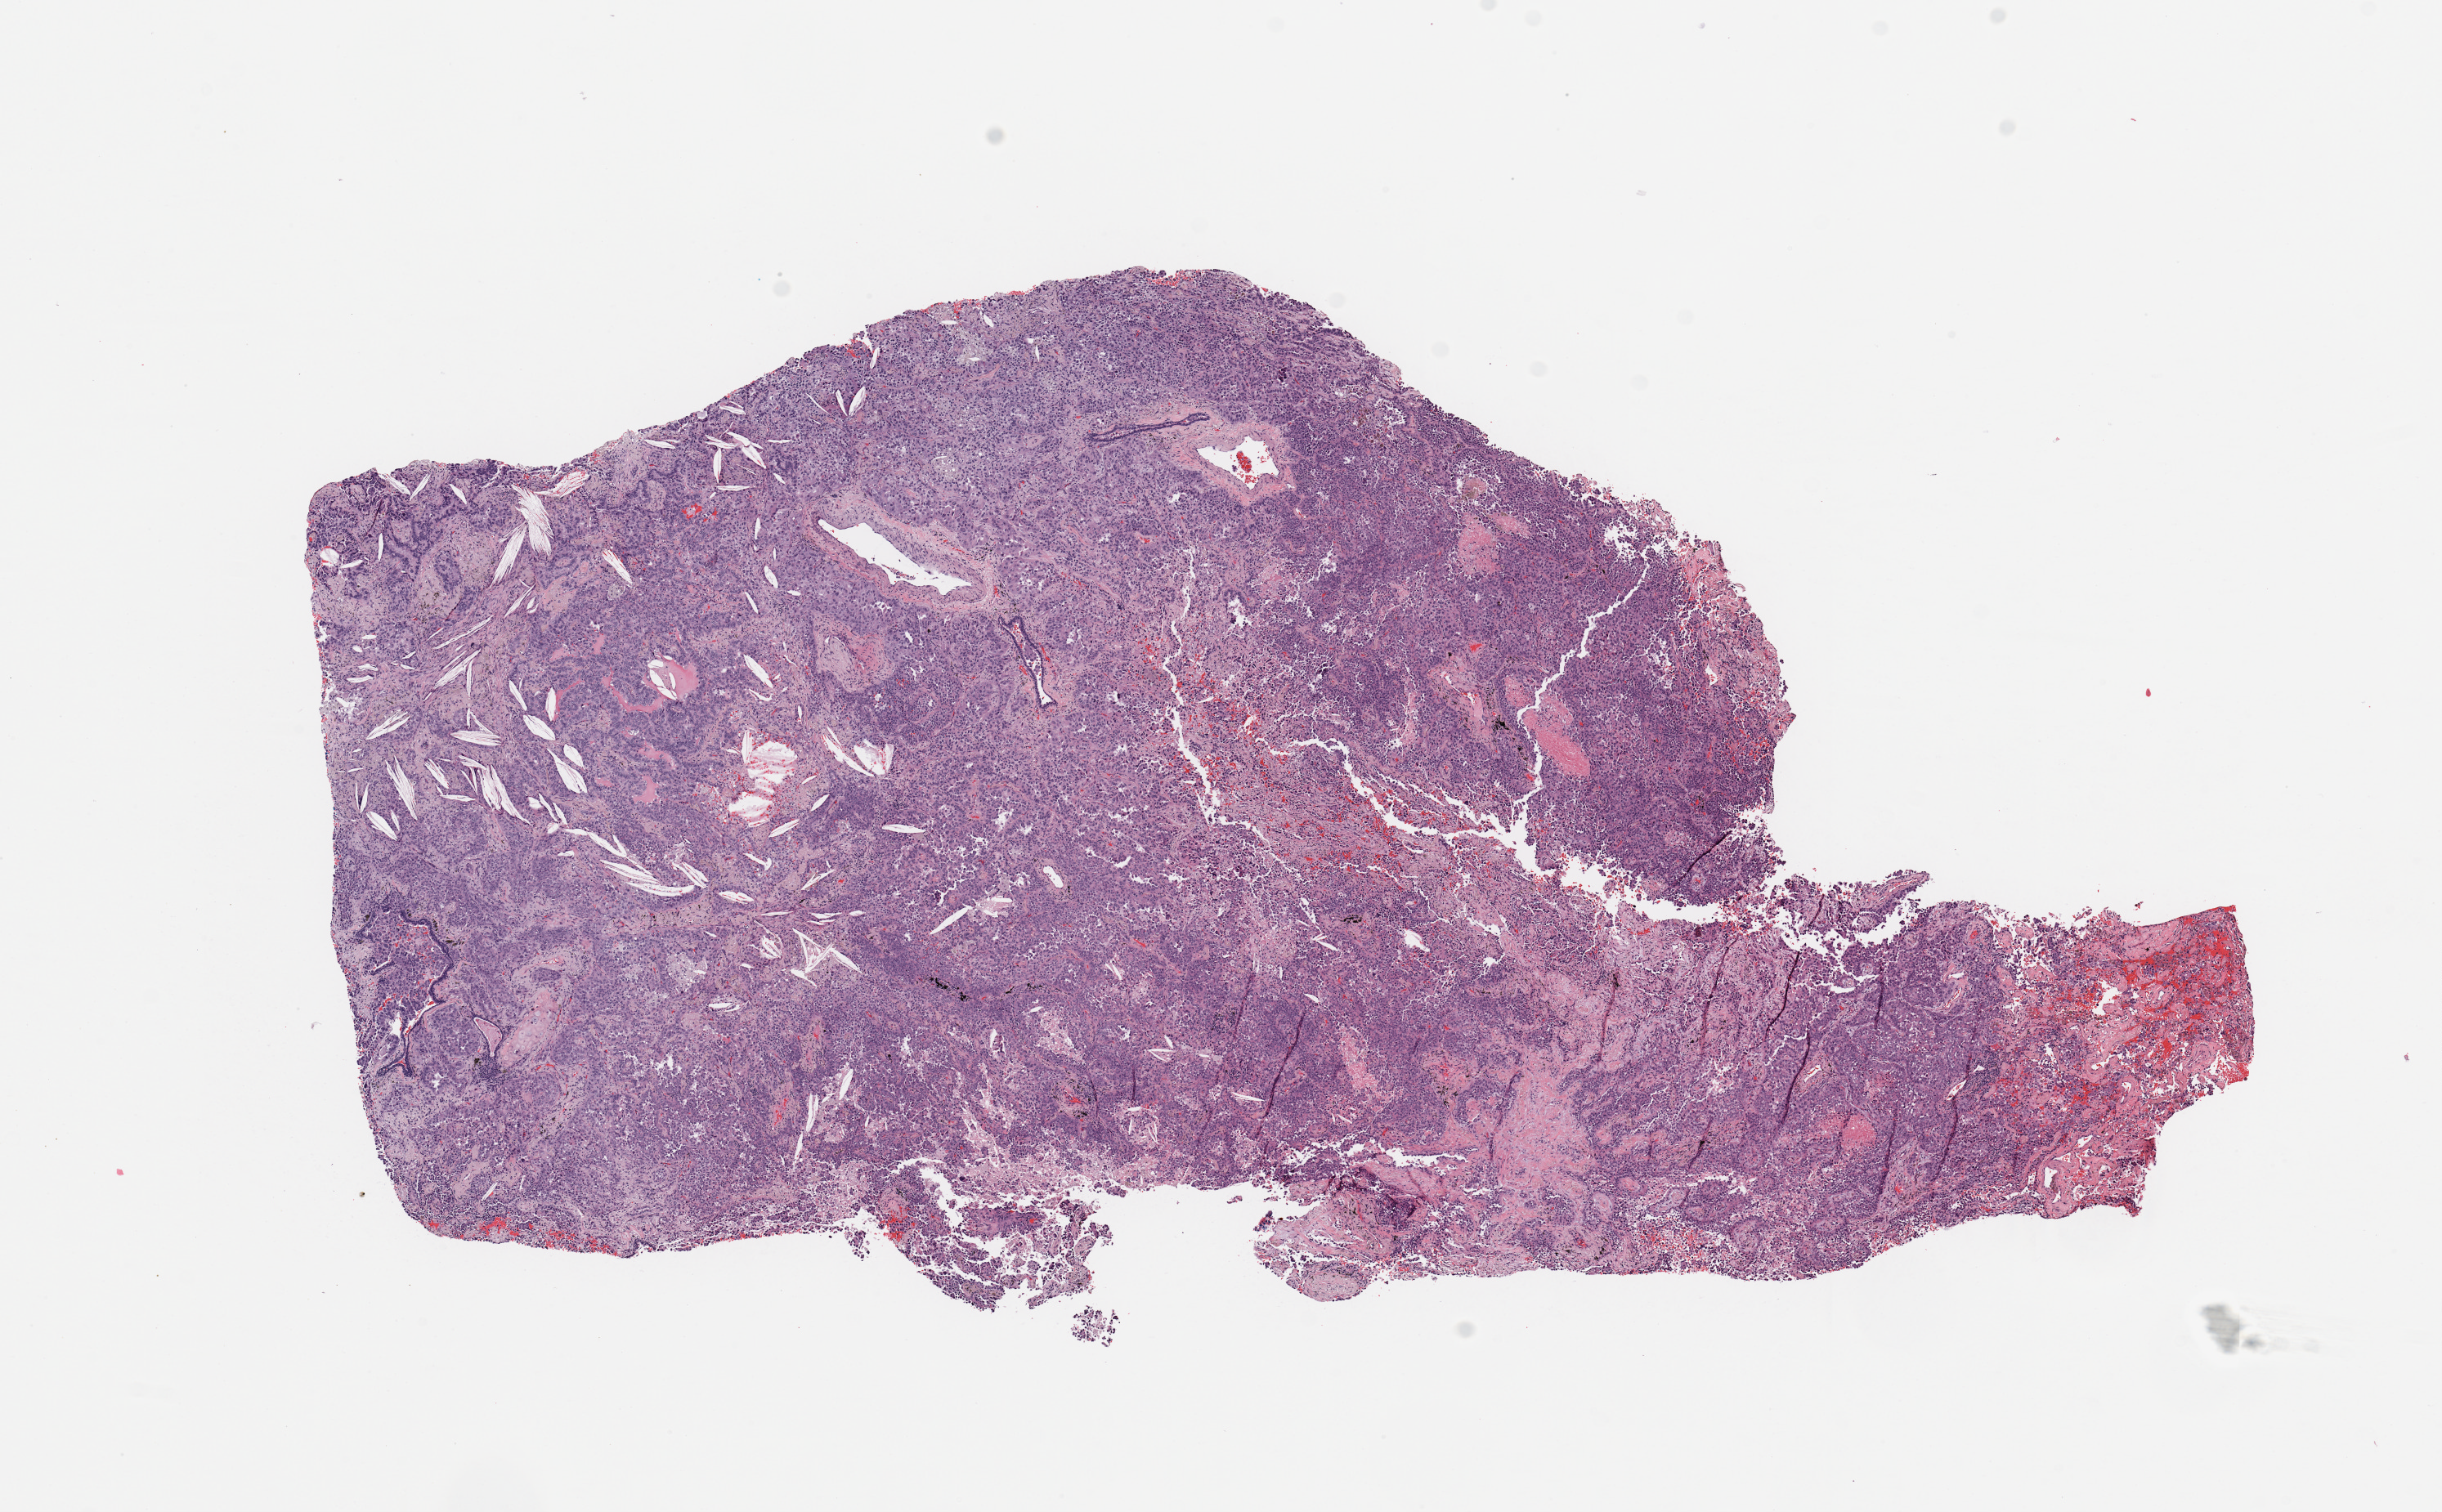
Whole-slide histology image, H&E — whole scanned area (about 11.8 x 7.3 mm, acquisition: 20x scan) shown as a low-resolution overview, tumour tissue sample, lung. Female, 62 y/o. Histologic grade: G3 (poorly differentiated).
Histologic diagnosis: Adenocarcinoma, NOS. AJCC pathologic stage: IIB. Primary tumour site (as recorded): right lower lobe.